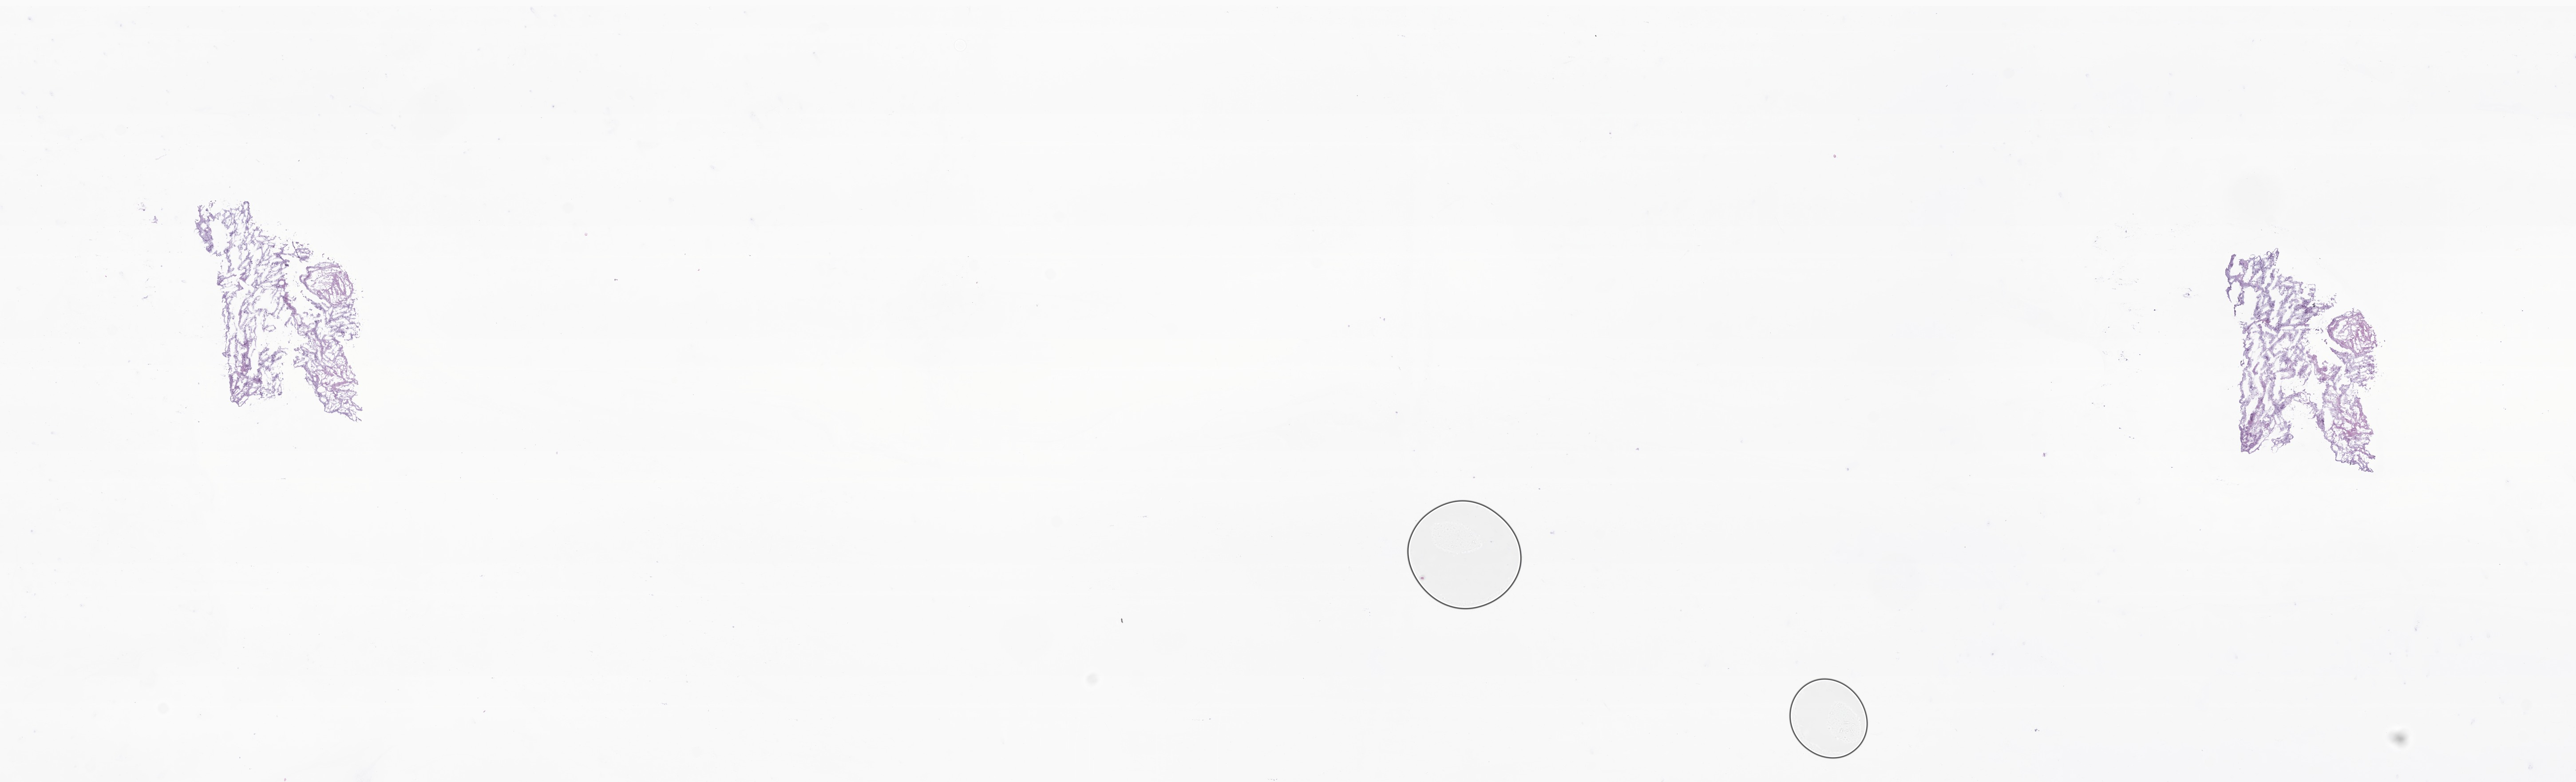
Whole-slide image, haematoxylin and eosin stain of tumor tissue from the cerebrum — shown as a low-resolution overview of the whole scanned area (about 24.5 x 7.4 mm); cryosection (OCT / tissue freezing medium). Patient female; age 86 months (7 years 2 months).
Diagnosis (ICD-O-3 morphology term): Pilocytic astrocytoma.